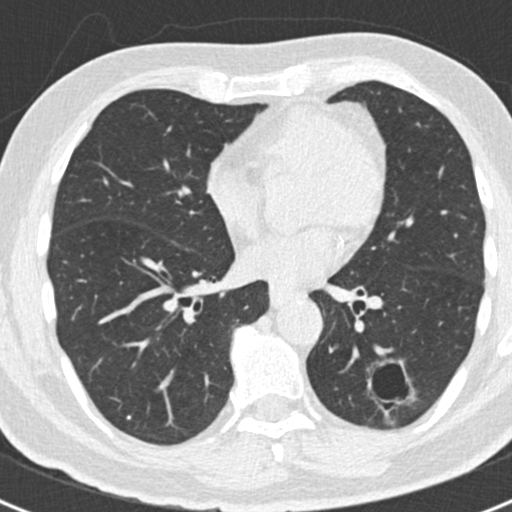
Low-dose screening chest CT, axial slice. Baseline annual screen. Lung window (W 1500 / L -600 HU). 2 mm slice thickness. Slice 95 of 188 in the series. Male participant, aged 66 years at enrolment. Former smoker at enrolment.
- Expert reader's lesion annotation, bounding box (x1, y1, x2, y2) in pixels: (346, 341, 421, 420).
- The exam's reader record, not a measurement of the box and not confirmed to be the same lesion: non-calcified nodule or mass ≥4 mm, left lower lobe, 43 × 27 mm, smooth margins.
- Official screen result: positive, change unspecified: nodule(s) >= 4 mm or enlarging nodule(s), mass(es), or other non-specific abnormalities suspicious for lung cancer.
- Later outcome: lung cancer diagnosed 801 days after this screen (after the third annual screen) — adenocarcinoma, NOS, left lower lobe, poorly differentiated (G3), stage IB (AJCC 6th edition), 38 mm at pathology.